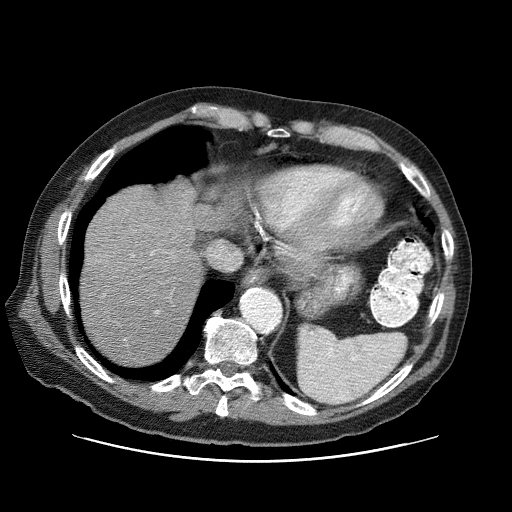
Contrast-enhanced abdominal CT (liver protocol), one axial slice. Position 65 of 87 along the scan axis. 120 kVp. One of 3 acquisitions stored at this slice position. Soft-tissue window (W 400 / L 40 HU). 2.5 mm slice thickness. 512 × 512 image matrix. Case-level facts recorded for this patient, not image findings: diagnosis: hepatocellular carcinoma (patient treated with transarterial chemoembolisation; whether this scan precedes or follows treatment is not stated here); TNM stage (as recorded): Stage-IIIA; Child-Pugh class: A; tumour differentiation: well differentiated; tumour nodularity: multinodular.
Annotated regions visible in this slice (semi-automatic segmentation, software-assisted and operator-edited):
- liver parenchyma outside the tumour (the mass and vessels are separate outlines, so this box may not span the whole liver): box from (x=80, y=186) to (x=242, y=366) px